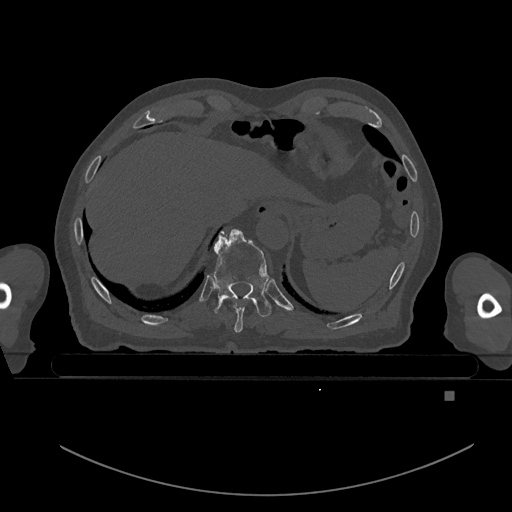
CT including the spine, one axial slice; position 108 of 969 along the scan axis; bone window (W 1800 / L 400 HU); 0.5 mm slice thickness; 512 × 512 image matrix, field of view 456 × 456 mm. Patient: male, 82 years. From the clinical record (not read from this slice): primary cancer: prostate.
Structures marked on this image (semi-automatic segmentation, software-assisted and operator-edited):
- T10 vertebra: box from (x=213, y=228) to (x=272, y=317) px
- T9 vertebra: (x=233, y=301)–(x=245, y=333)